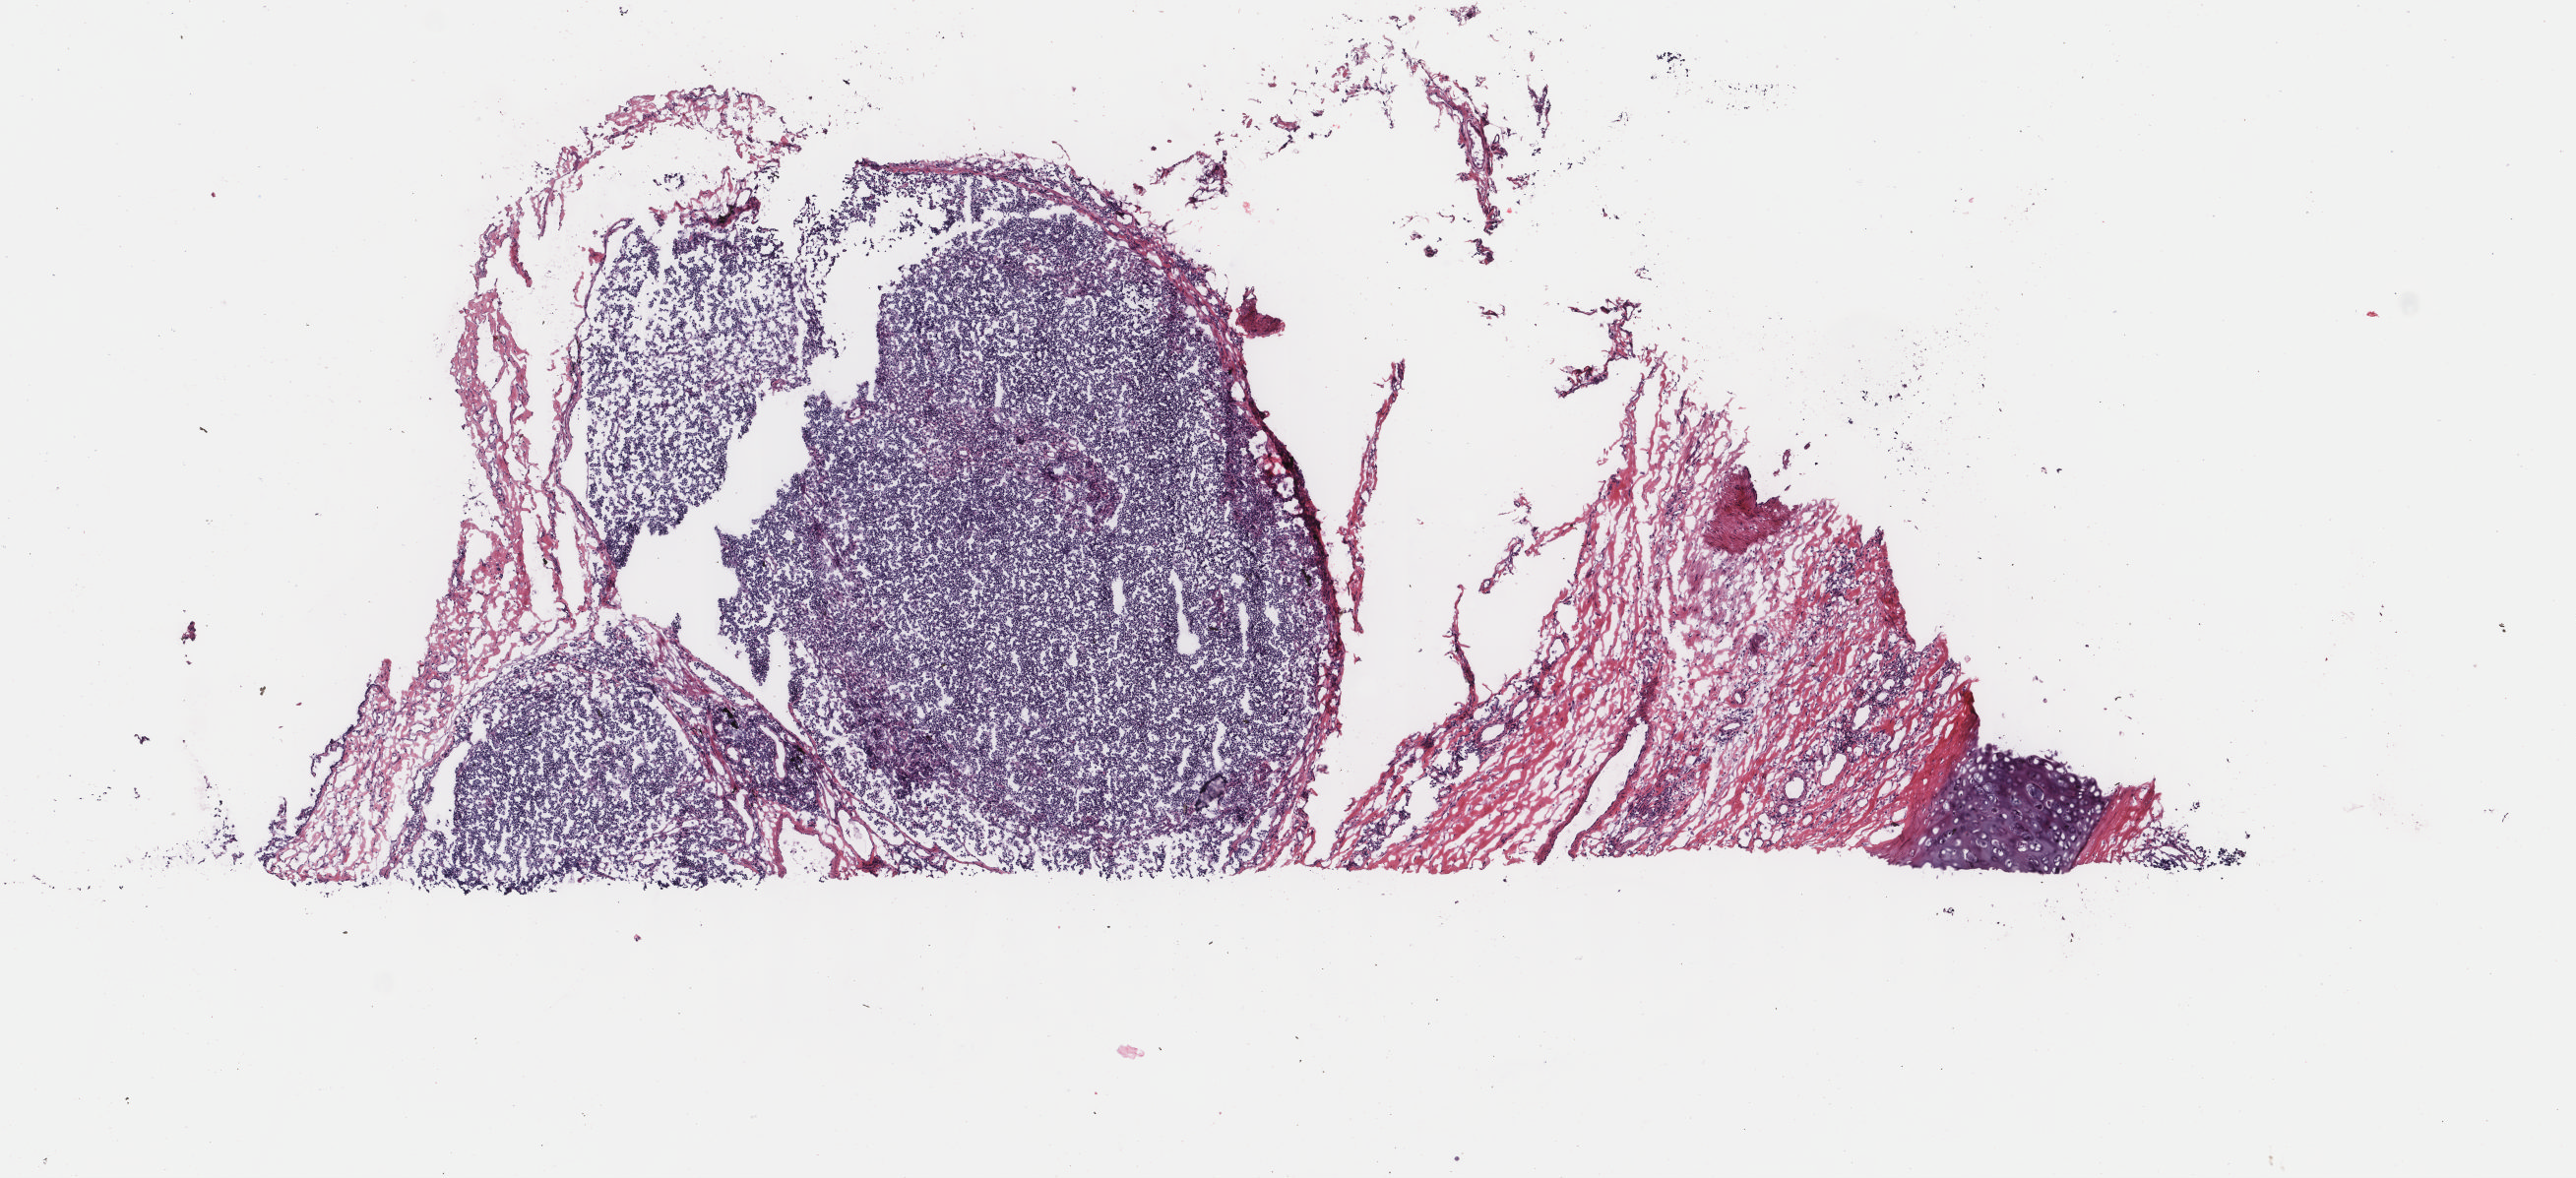
Digitized Hematoxylin and eosin (H&E) stained tissue section (whole slide), whole scanned area (about 10.4 x 4.8 mm, from a 40x scan) shown as a low-resolution overview, frozen section from the top of the tissue portion, lung, primary tumour sample. Male, age 61 years at initial diagnosis. Composition of this section per pathologist review: tumour cells 70%, tumour nuclei 75%, normal cells 30%, stromal cells 0%, necrosis 0%. Inflammatory infiltration, as recorded: lymphocyte infiltration 2%, monocyte infiltration 0%, neutrophil infiltration 0%.
AJCC pathologic stage: IB (7th edition). TNM: T2a N0 M0. Diagnosis: Squamous cell carcinoma, large cell, nonkeratinizing, NOS (lower lobe, lung).